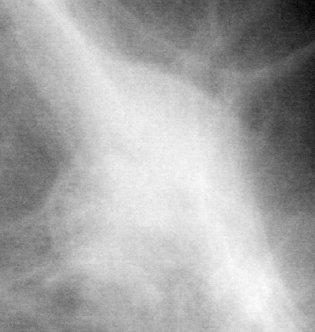
Region of interest cut from a scanned film mammogram (one marked finding), left breast, MLO view, BI-RADS breast density category 1 (scale 1–4).
Finding: mass, shape lobulated, margins obscured; BI-RADS assessment category 3; subtlety rating 3 on a 1 (subtle) to 5 (obvious) scale; pathology (as recorded): malignant.